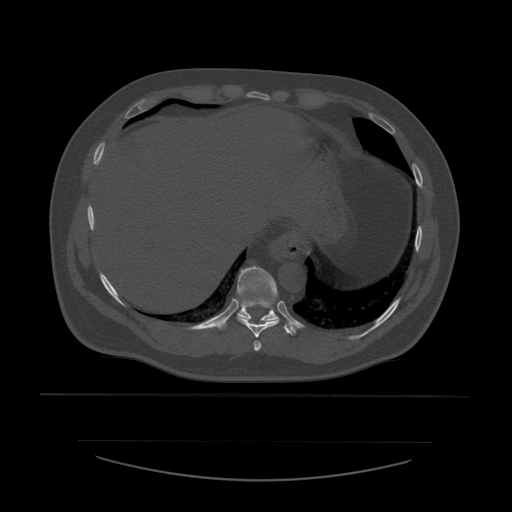
CT including the spine, one axial slice; position 309 of 532 along the scan axis; reconstruction kernel STANDARD; bone window (W 1800 / L 400 HU); 1.25 mm slice thickness; 512 × 512 image matrix. Patient age 44 years. From the clinical record (not read from this slice): primary cancer: soft tissue sarcoma.
Outlined on this slice (semi-automatically segmented with operator editing):
- T10 vertebra: box from (x=219, y=266) to (x=295, y=336) px
- T8 vertebra: (x=254, y=341)–(x=262, y=353)
- T9 vertebra: (x=237, y=268)–(x=280, y=338)